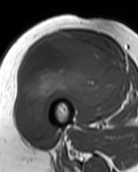
MRI of an extremity soft-tissue mass, one axial slice; slice 52 of 99 in the series (ordered by position); MR volume resampled by the dataset authors to the PET/CT grid (not the native acquisition matrix); 3.27 mm slice thickness; 138 × 172 image matrix, field of view 135 × 168 mm. Female patient. From the clinical record (not read from this slice): histological type: pleiomorphic undifferentiated sarcoma; grade: high; site of the primary tumour: right quadricep.
Outlined on this slice (expert contour drawn on MRI and transferred to this co-registered scan by the dataset authors):
- gross tumour volume including surrounding oedema: bounding box [x1, y1, x2, y2] px = [16, 32, 125, 138]
- gross tumour volume (mass): [16, 32, 125, 138]